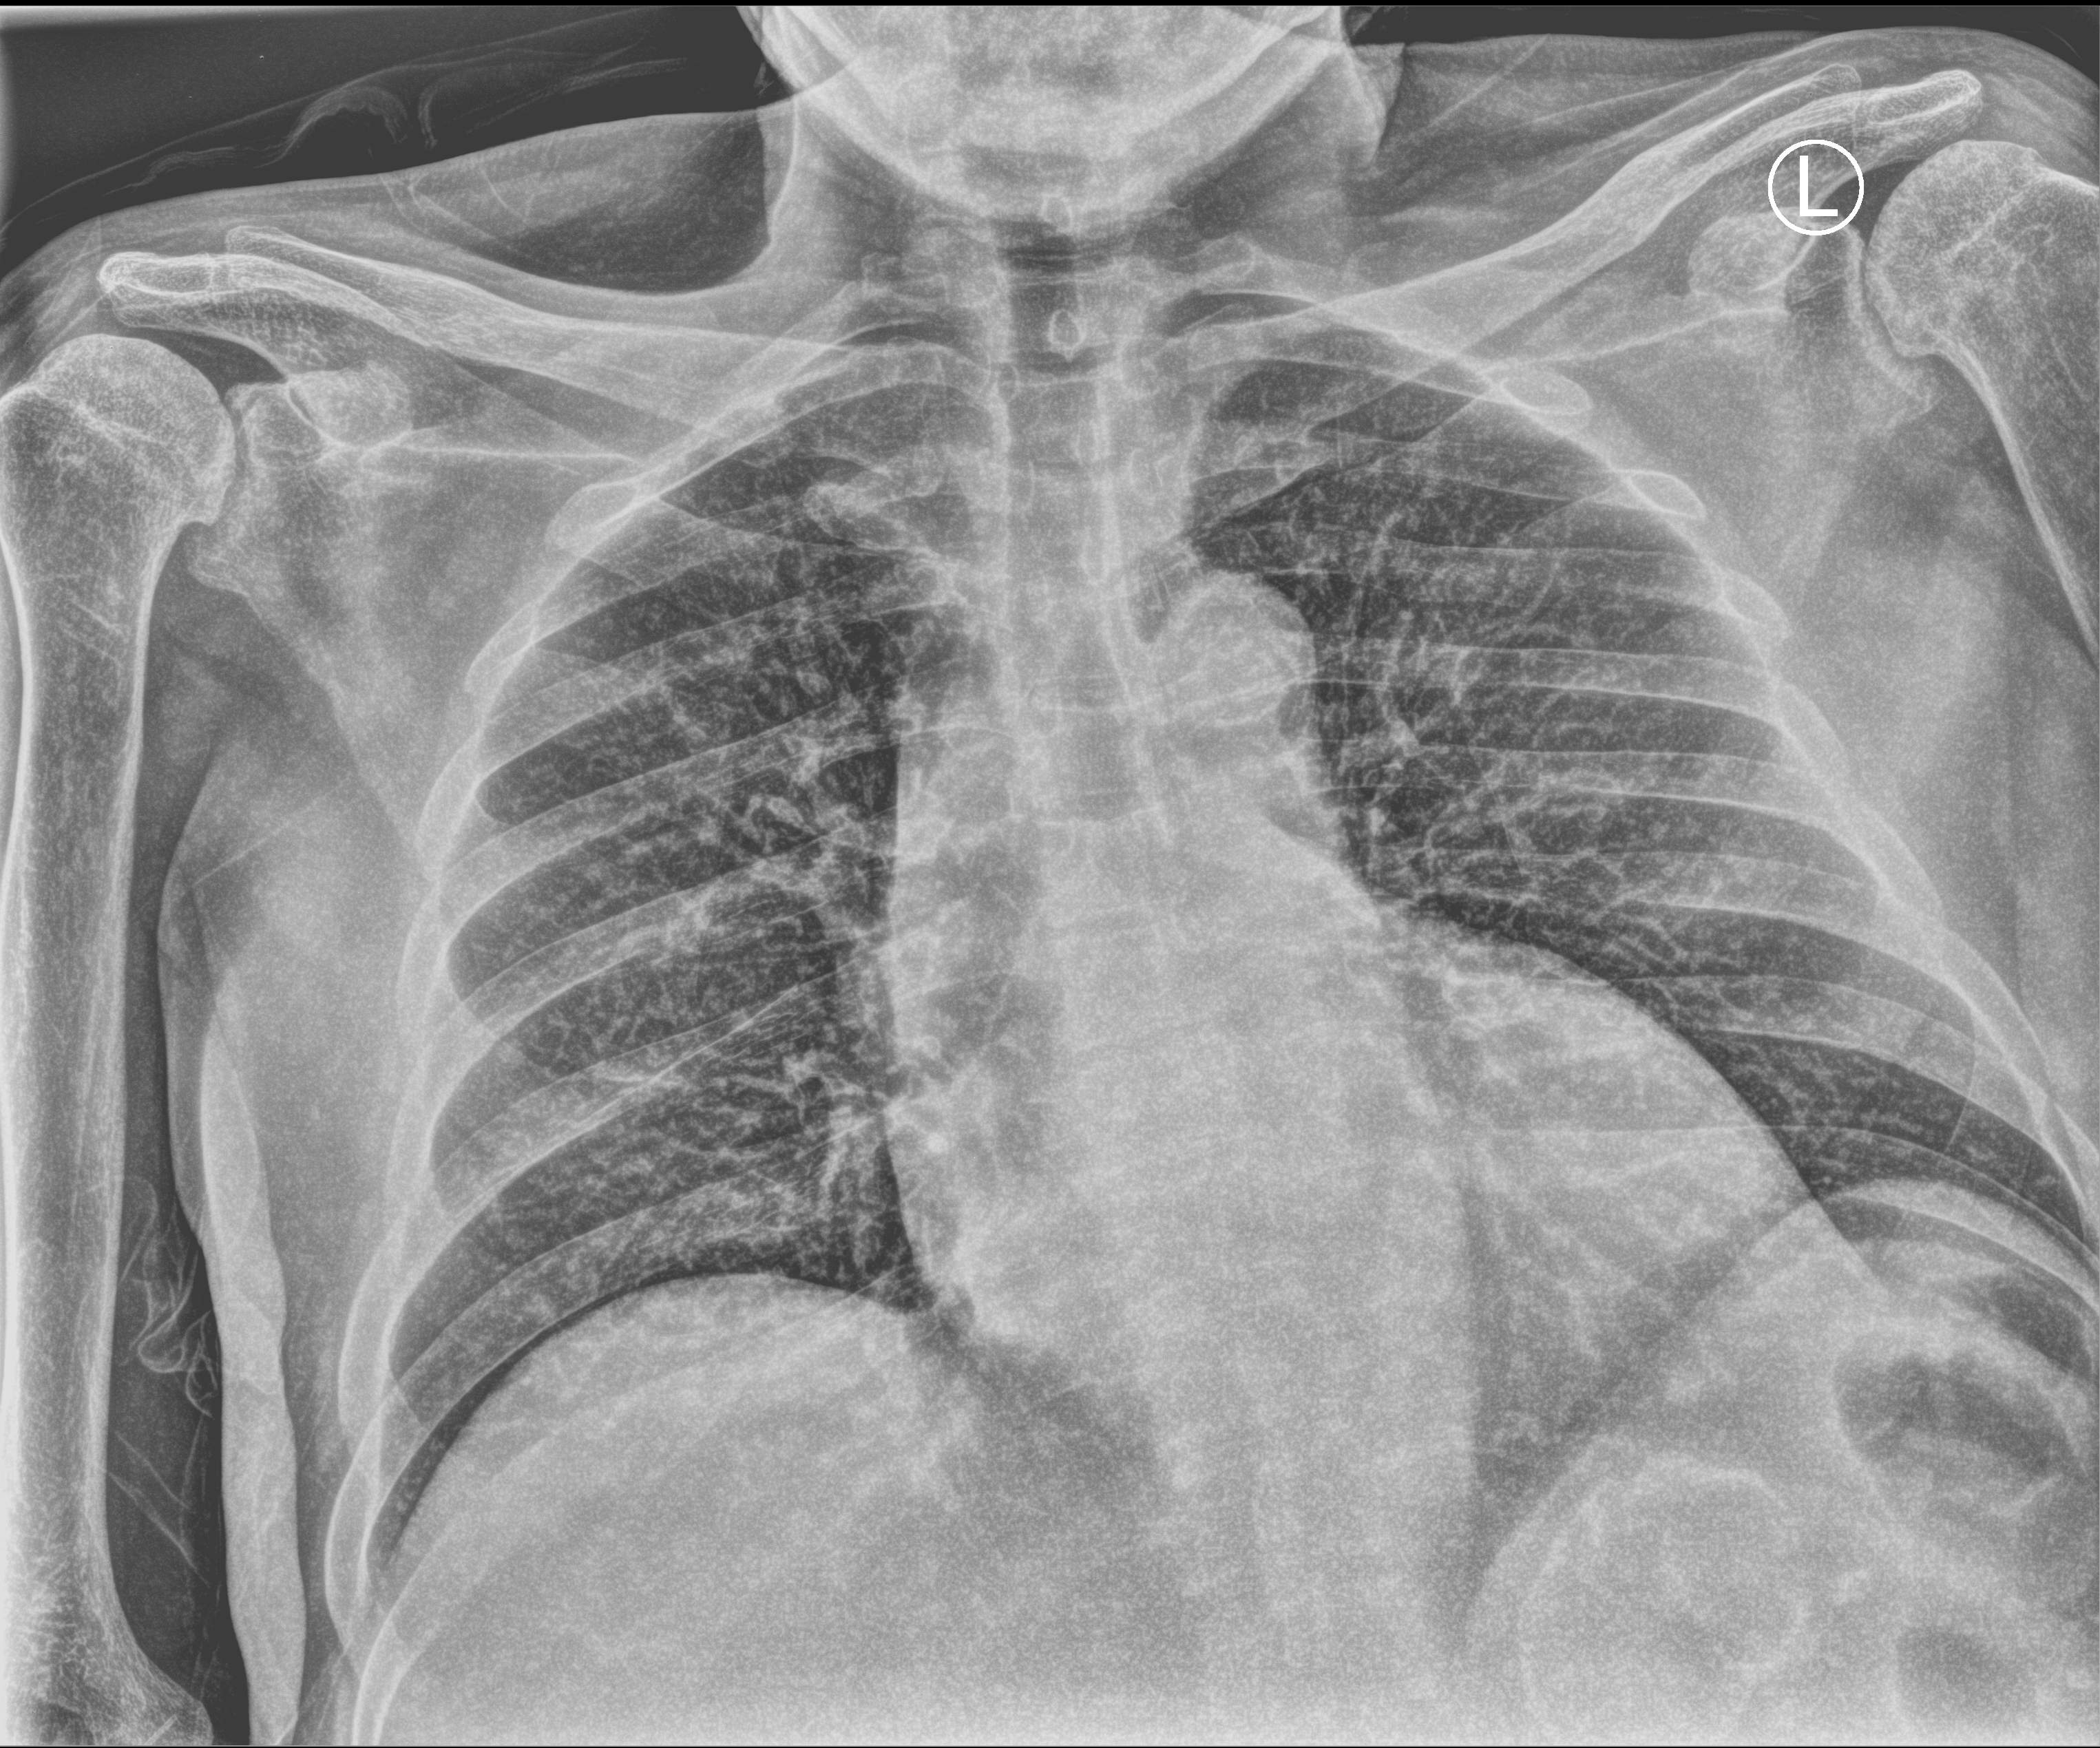
Portable chest radiograph, anteroposterior (AP) projection. Male patient hospitalised with COVID-19, age 60–74 years.
Admission-level facts for this patient (not findings on this image; timing relative to this image not recorded):
- other chronic lung disease (admission record): no